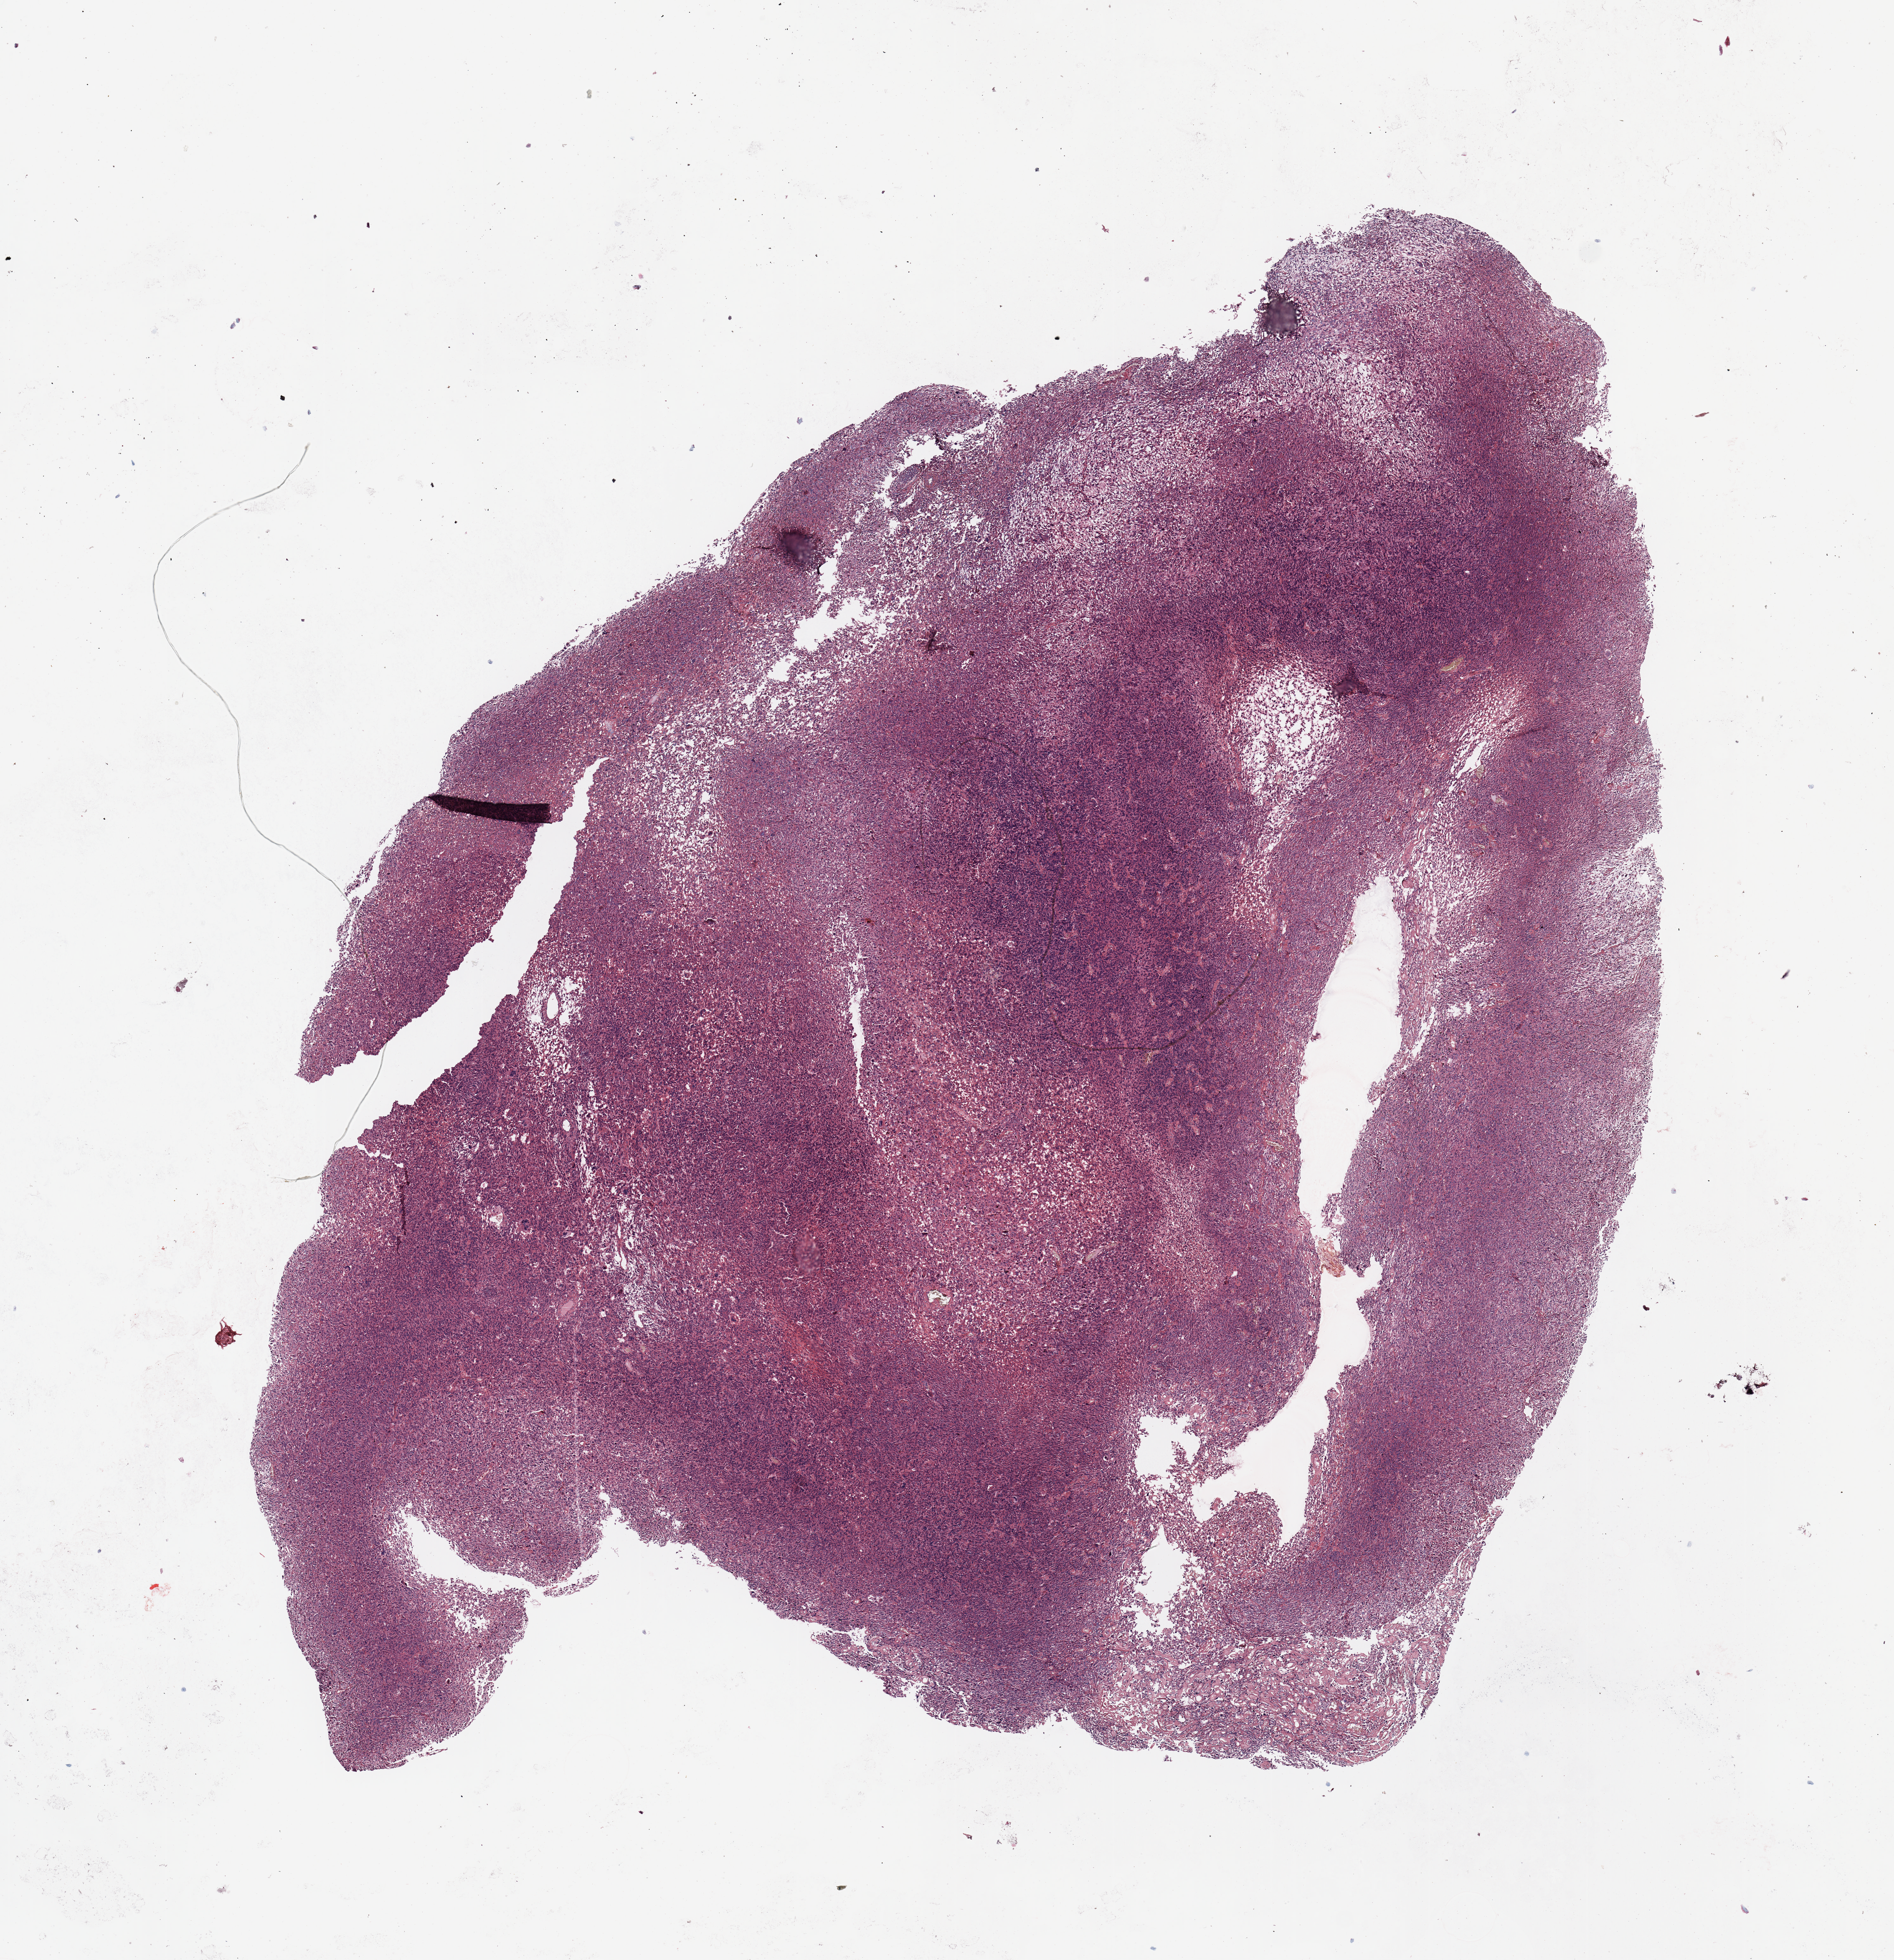
Whole-slide histology image, H&E-stained, whole scanned area (about 11.8 x 12.2 mm, slide scanned at 20x) shown as a low-resolution overview; tumour tissue sample. 58-year-old female patient.
• primary tumour site (as recorded): upper extremity
• patient diagnosis (cohort enrolment): sarcoma (site not recorded at cohort level)